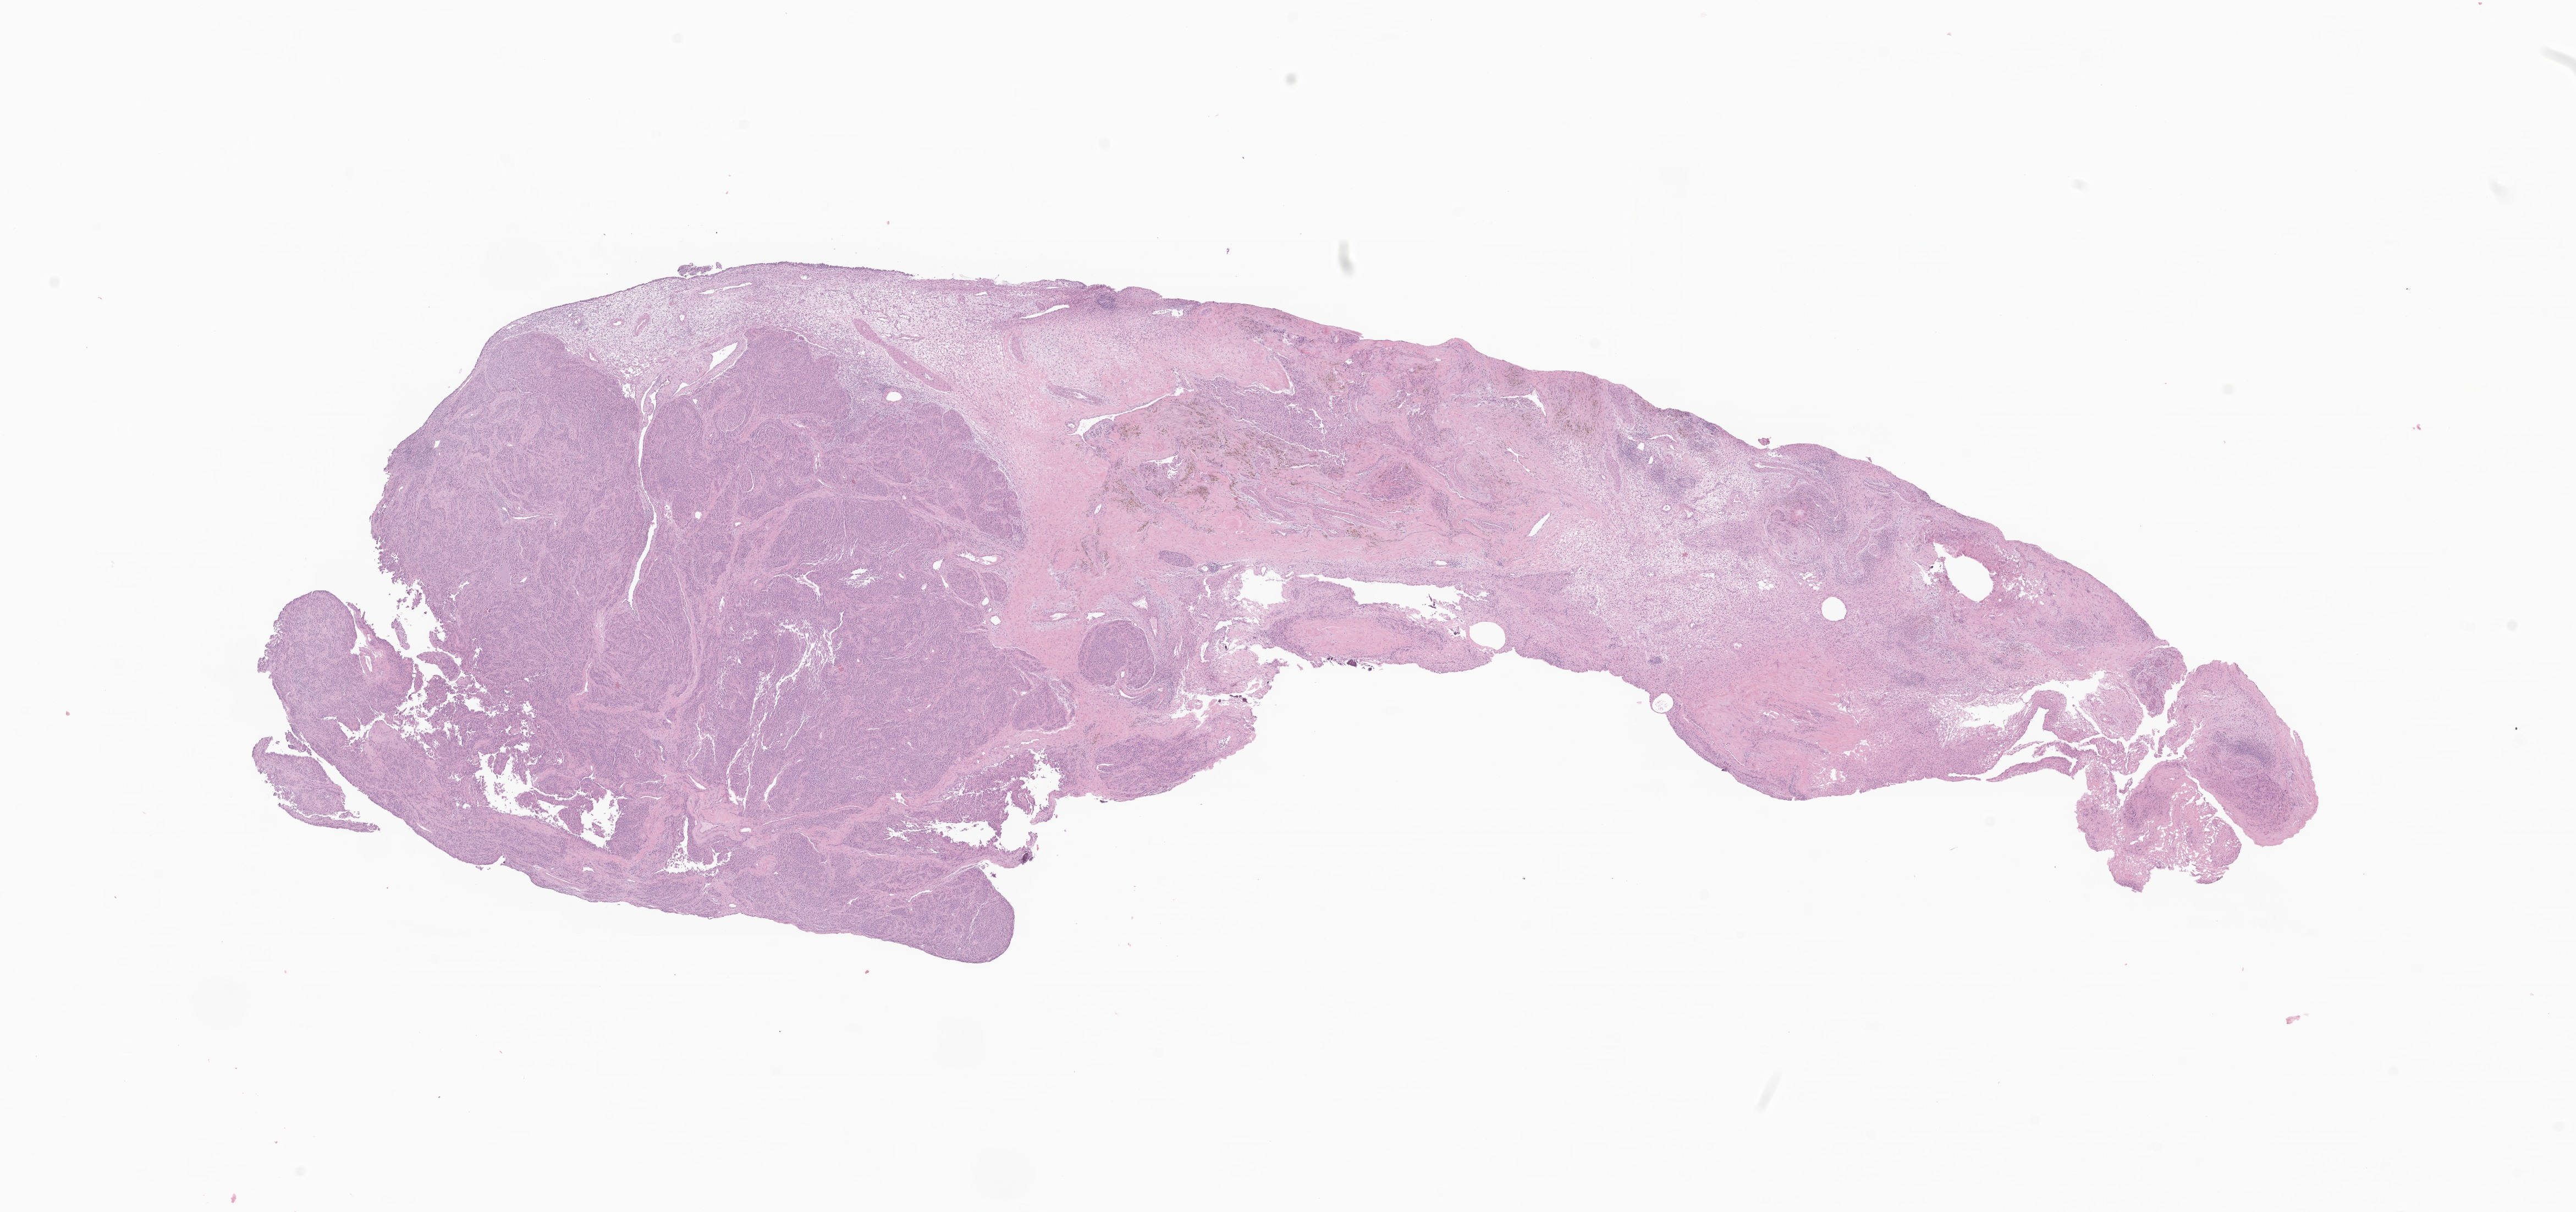
H&E whole-slide image of tumor tissue from the brain, whole scanned area (about 19.7 x 9.3 mm) shown as a low-resolution overview. Formalin-fixed, paraffin-embedded (FFPE) tissue. Patient female; age 245 months (20 years 5 months).
- recorded diagnosis: Meningioma, NOS